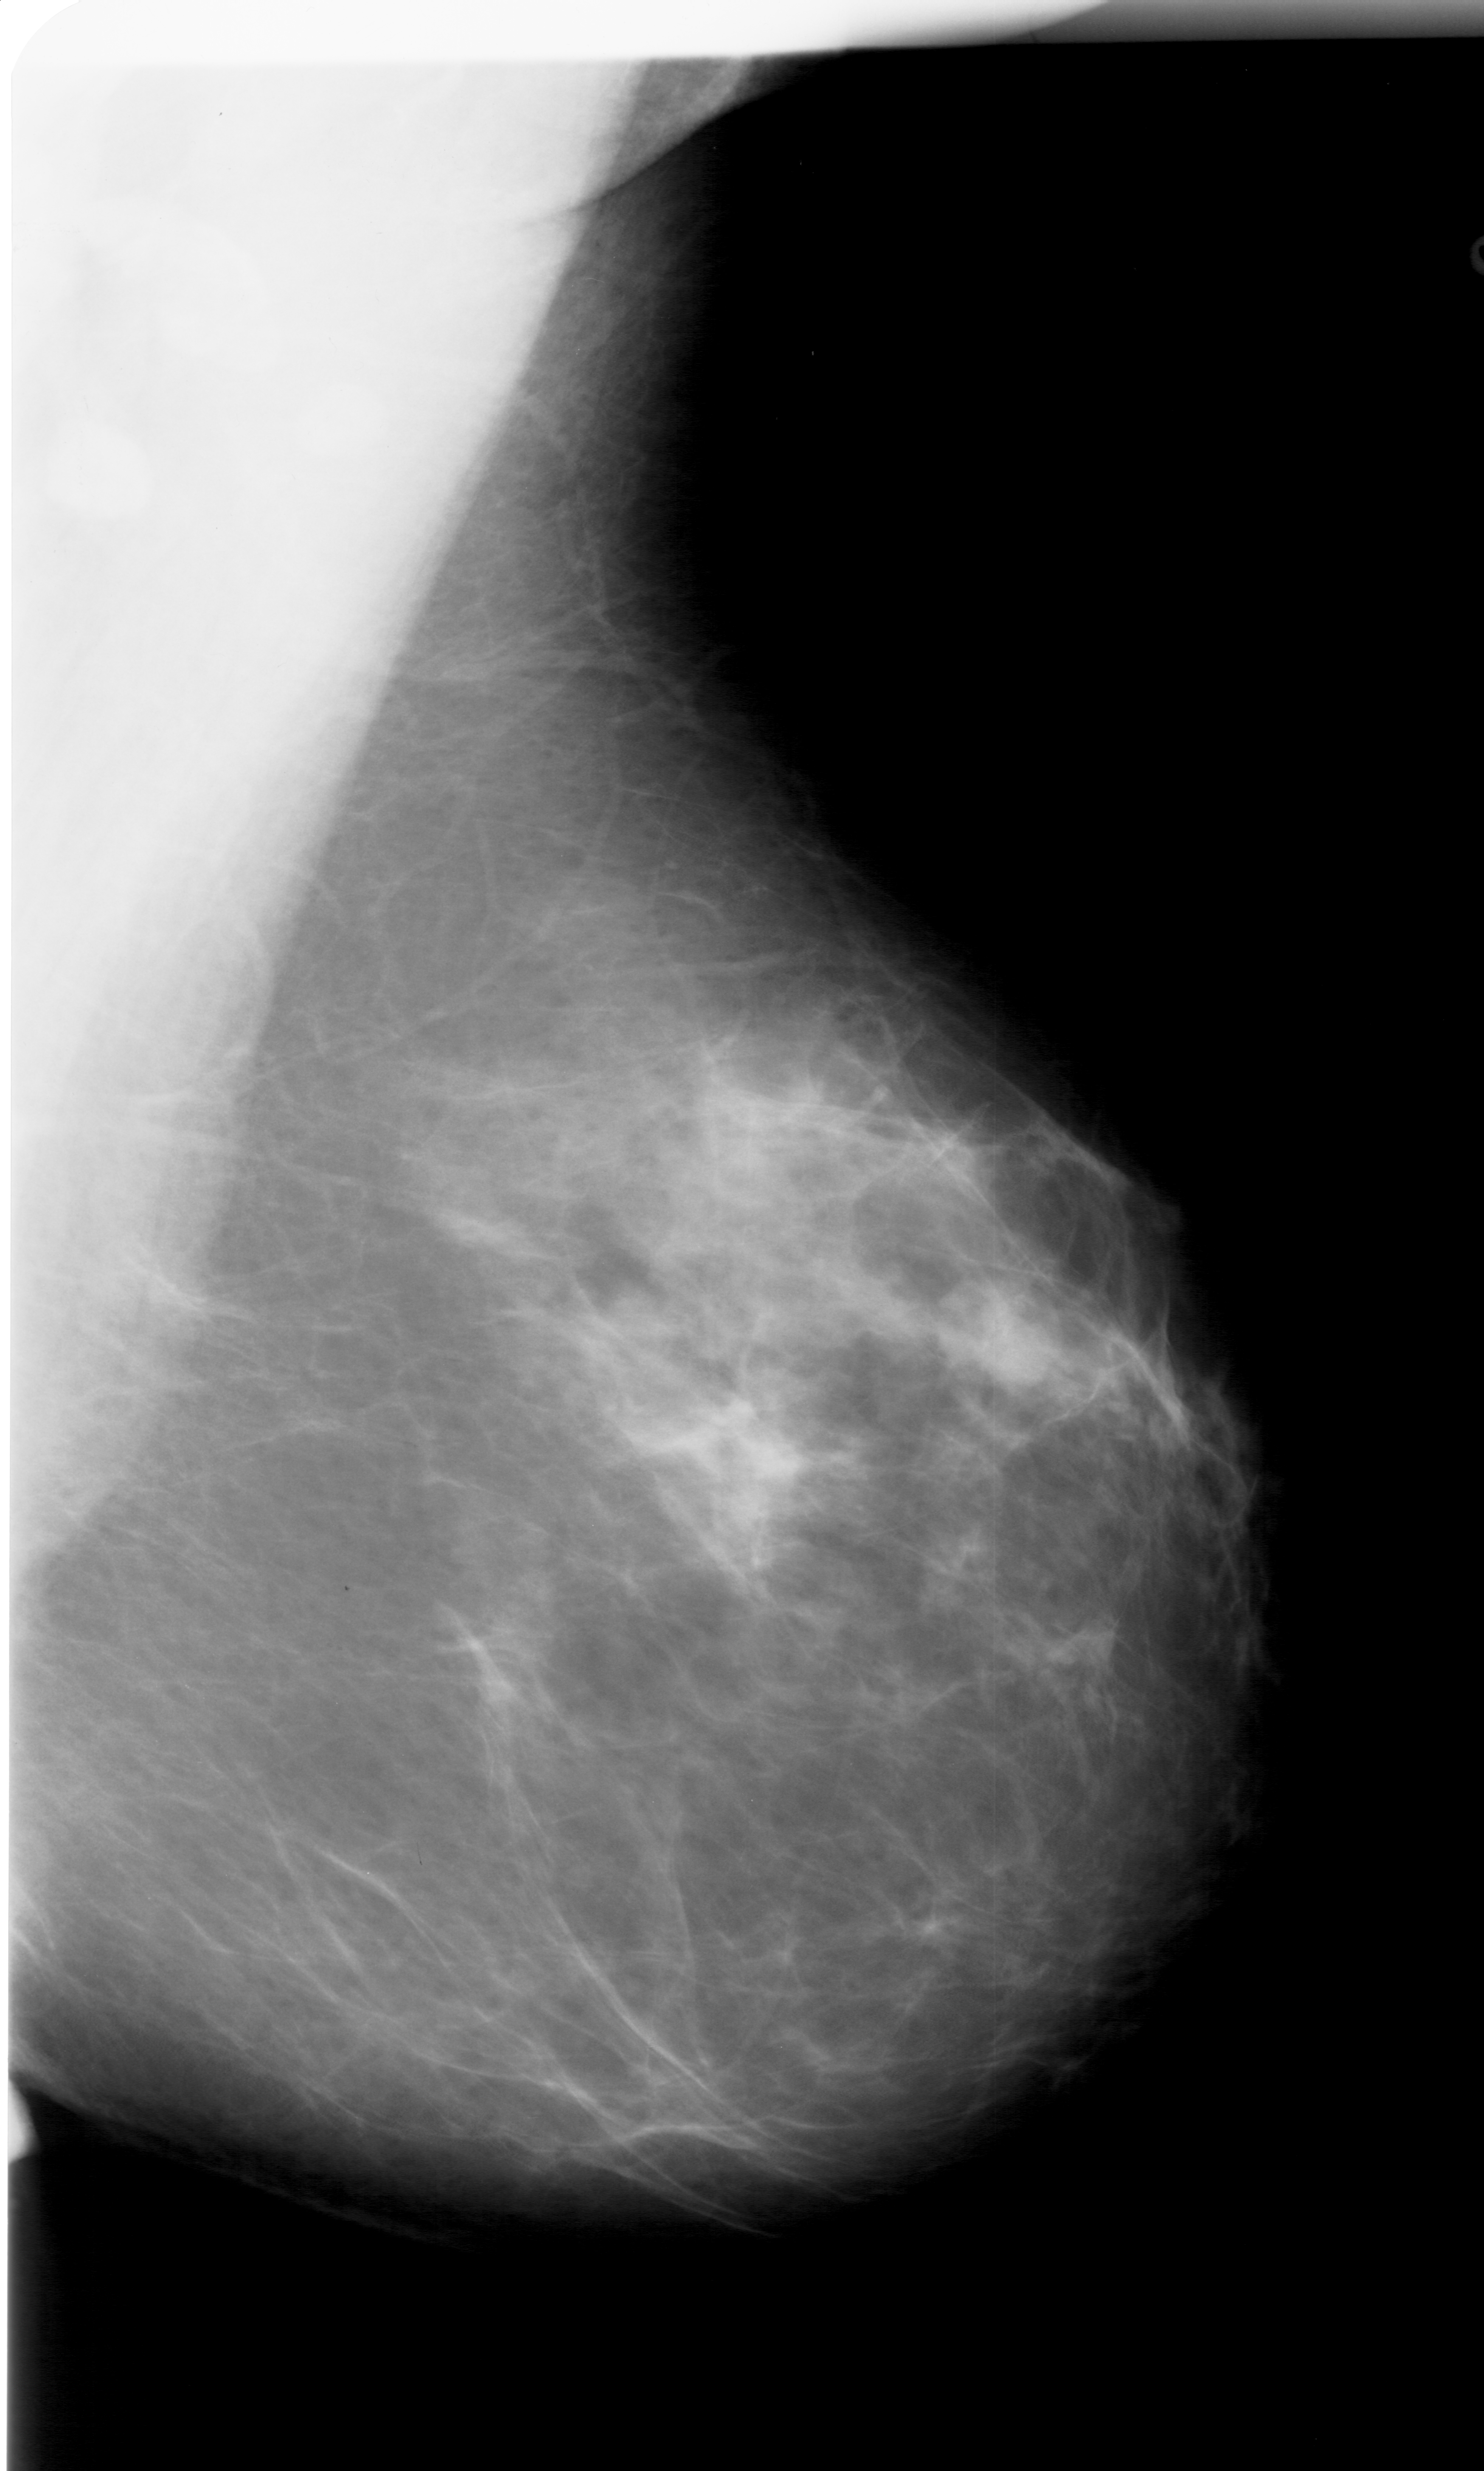
Digitized screen-film mammogram; right breast; mediolateral oblique (MLO) view; breast composition: scattered fibroglandular densities (BI-RADS density category 2 of 4).
Marked findings (only marked abnormalities are described; nothing is implied about the rest of the image): mass, shape oval, margins circumscribed; BI-RADS assessment category 3; pathology (as recorded): benign.